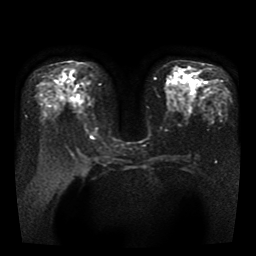
Breast MRI, one axial slice; position 20 of 41 along the scan axis; diffusion-weighted series; image 2 of 4 stored at this slice position (different b-values; order by instance number); 1.5 T; 5 mm slice thickness; 256 × 256 image matrix, field of view 330 × 330 mm. Female patient.
Structures marked on this image (outlined manually by an expert reader):
- tumour on diffusion-weighted imaging: bounding box <169,92,177,98> (left, top, right, bottom; pixels)